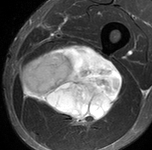
MRI of an extremity soft-tissue mass, one axial slice. Slice 57 of 90 in the series (ordered by position). STIR. MR volume resampled by the dataset authors to the PET/CT grid (not the native acquisition matrix). 3.27 mm slice thickness. 152 × 150 image matrix. Male patient. From the clinical record (not read from this slice): histological type: undifferentiated pleomorphic liposarcoma; grade: high; site of the primary tumour: left thigh.
Outlined on this slice (expert contour drawn on MRI and transferred to this co-registered scan by the dataset authors):
- gross tumour volume including surrounding oedema: box from (x=20, y=44) to (x=124, y=127) px
- gross tumour volume (mass): (x=20, y=44)–(x=124, y=125)